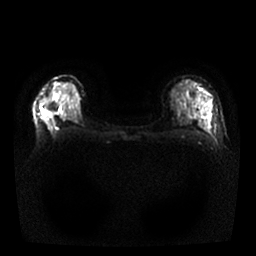
Breast MRI, one axial slice; diffusion-weighted series; image 2 of 4 stored at this slice position (different b-values; order by instance number); 1.5 T; 4 mm slice thickness; 256 × 256 image matrix, field of view 330 × 330 mm. Female patient.
Structures marked on this image (outlined manually by an expert reader):
- tumour on diffusion-weighted imaging: bounding box [x1, y1, x2, y2] px = [42, 110, 47, 116]